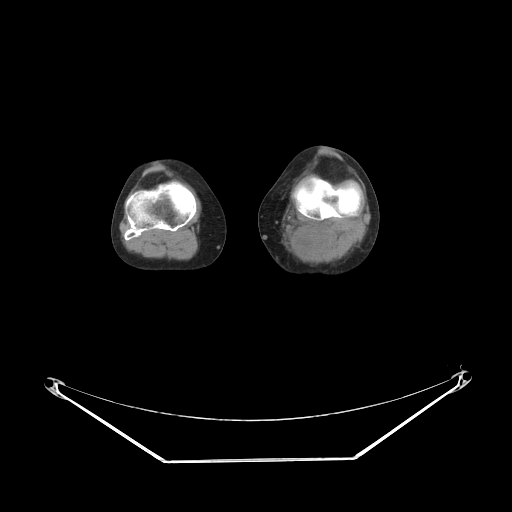
CT of an extremity soft-tissue mass (from a PET/CT study), one axial slice; position 163 of 223 along the scan axis; reconstruction kernel STANDARD; soft-tissue window (W 400 / L 40 HU); 3.75 mm slice thickness; 512 × 512 image matrix, field of view 500 × 500 mm. Female patient. Case-level facts recorded for this patient, not image findings: histological type: extraskeletal high grade osteogenic sarcoma; grade: high; site of the primary tumour: left calf.
Outlined on this slice (expert contour drawn on MRI and transferred to this co-registered scan by the dataset authors):
- gross tumour volume (mass): box from (x=295, y=231) to (x=321, y=254) px